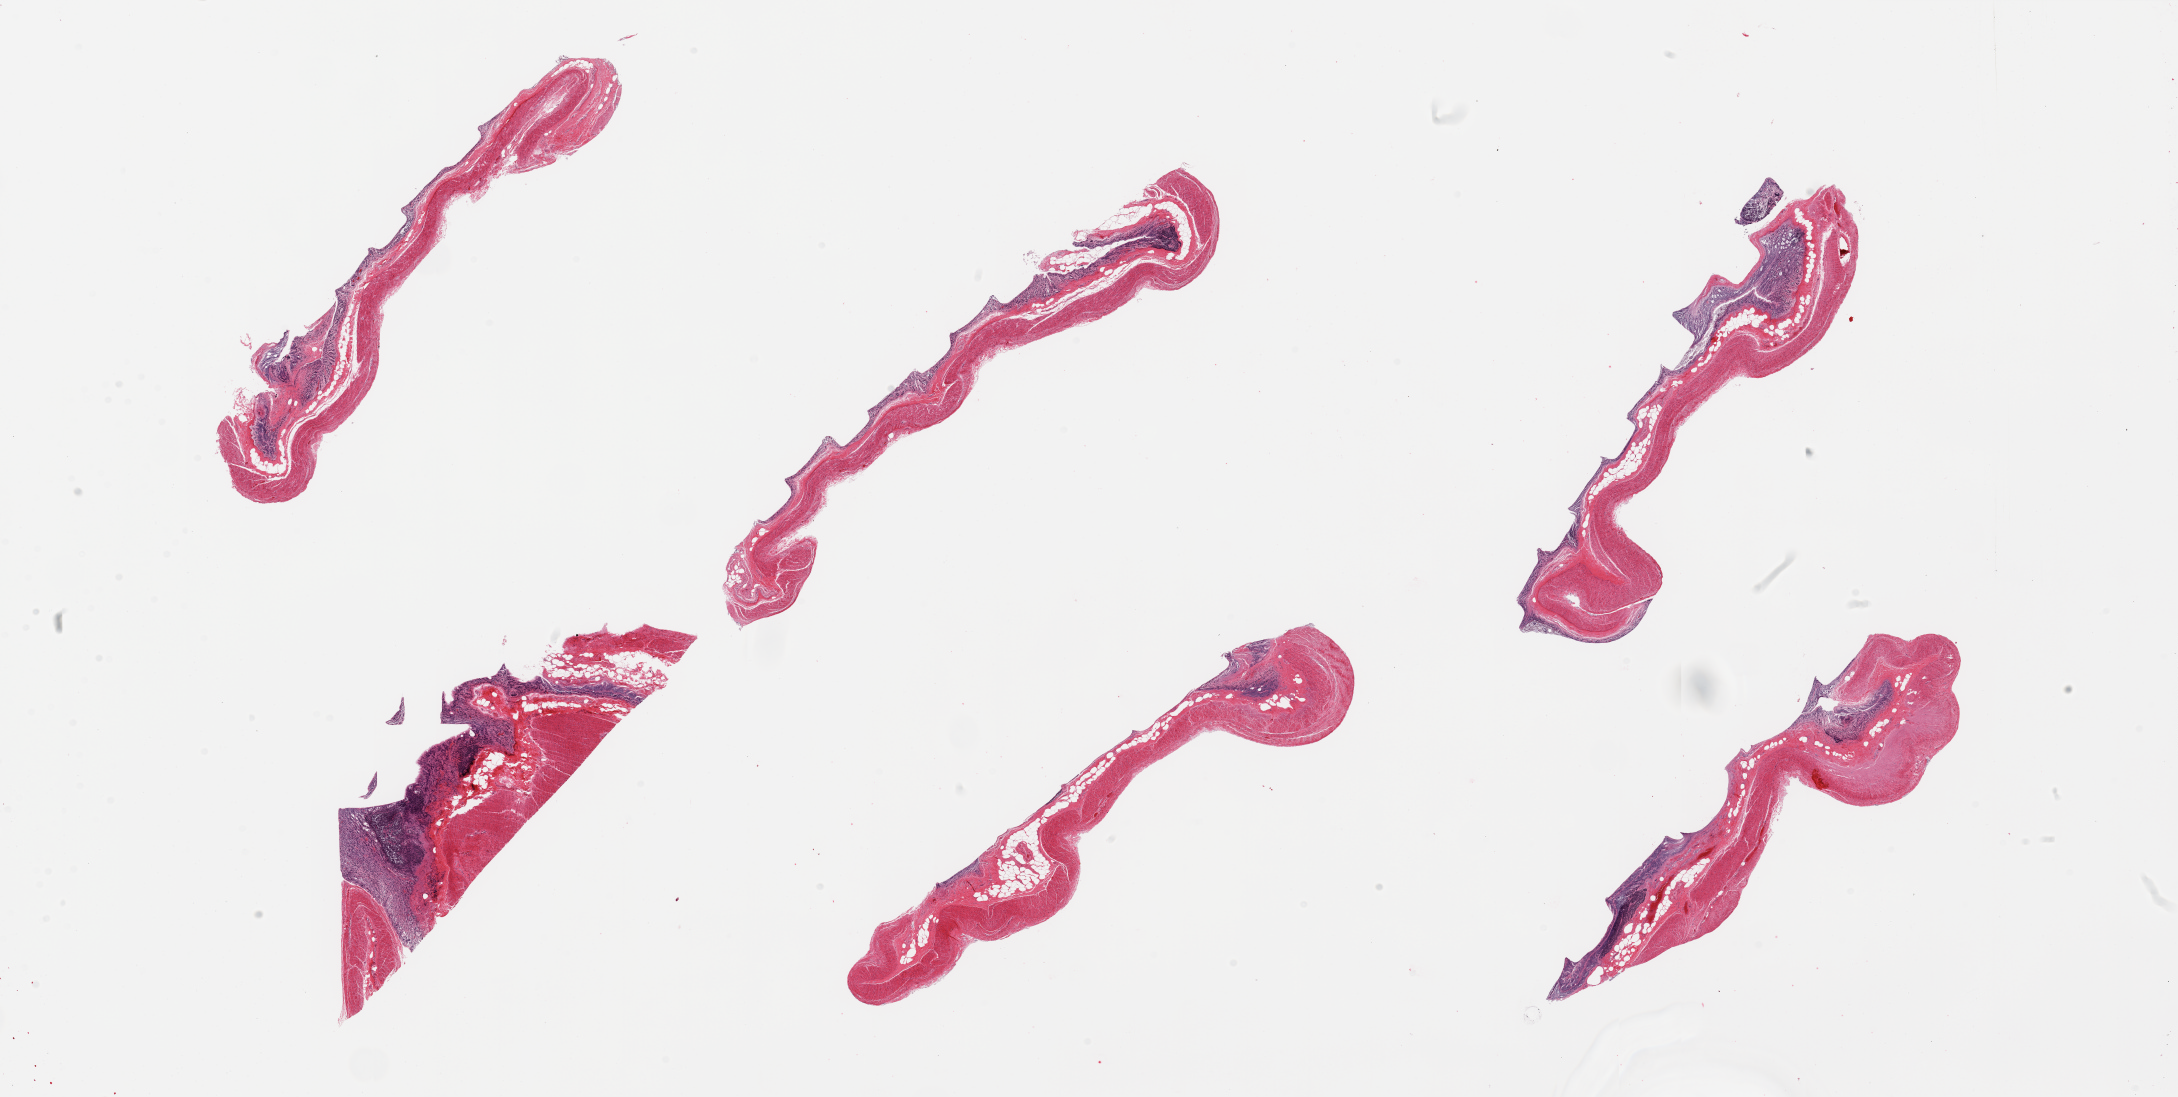
Digitized haematoxylin and eosin-stained section, brightfield — whole scanned area (about 34.5 x 17.4 mm) shown as a low-resolution overview. PAXgene-fixed paraffin-embedded (PFPE) section. Sampled site (target tissue): transverse colon. Donor tissue sample. Male donor.
Reviewer comment on this tissue sample: 6 pieces; mucosa autolyzed, muscularis preserved.